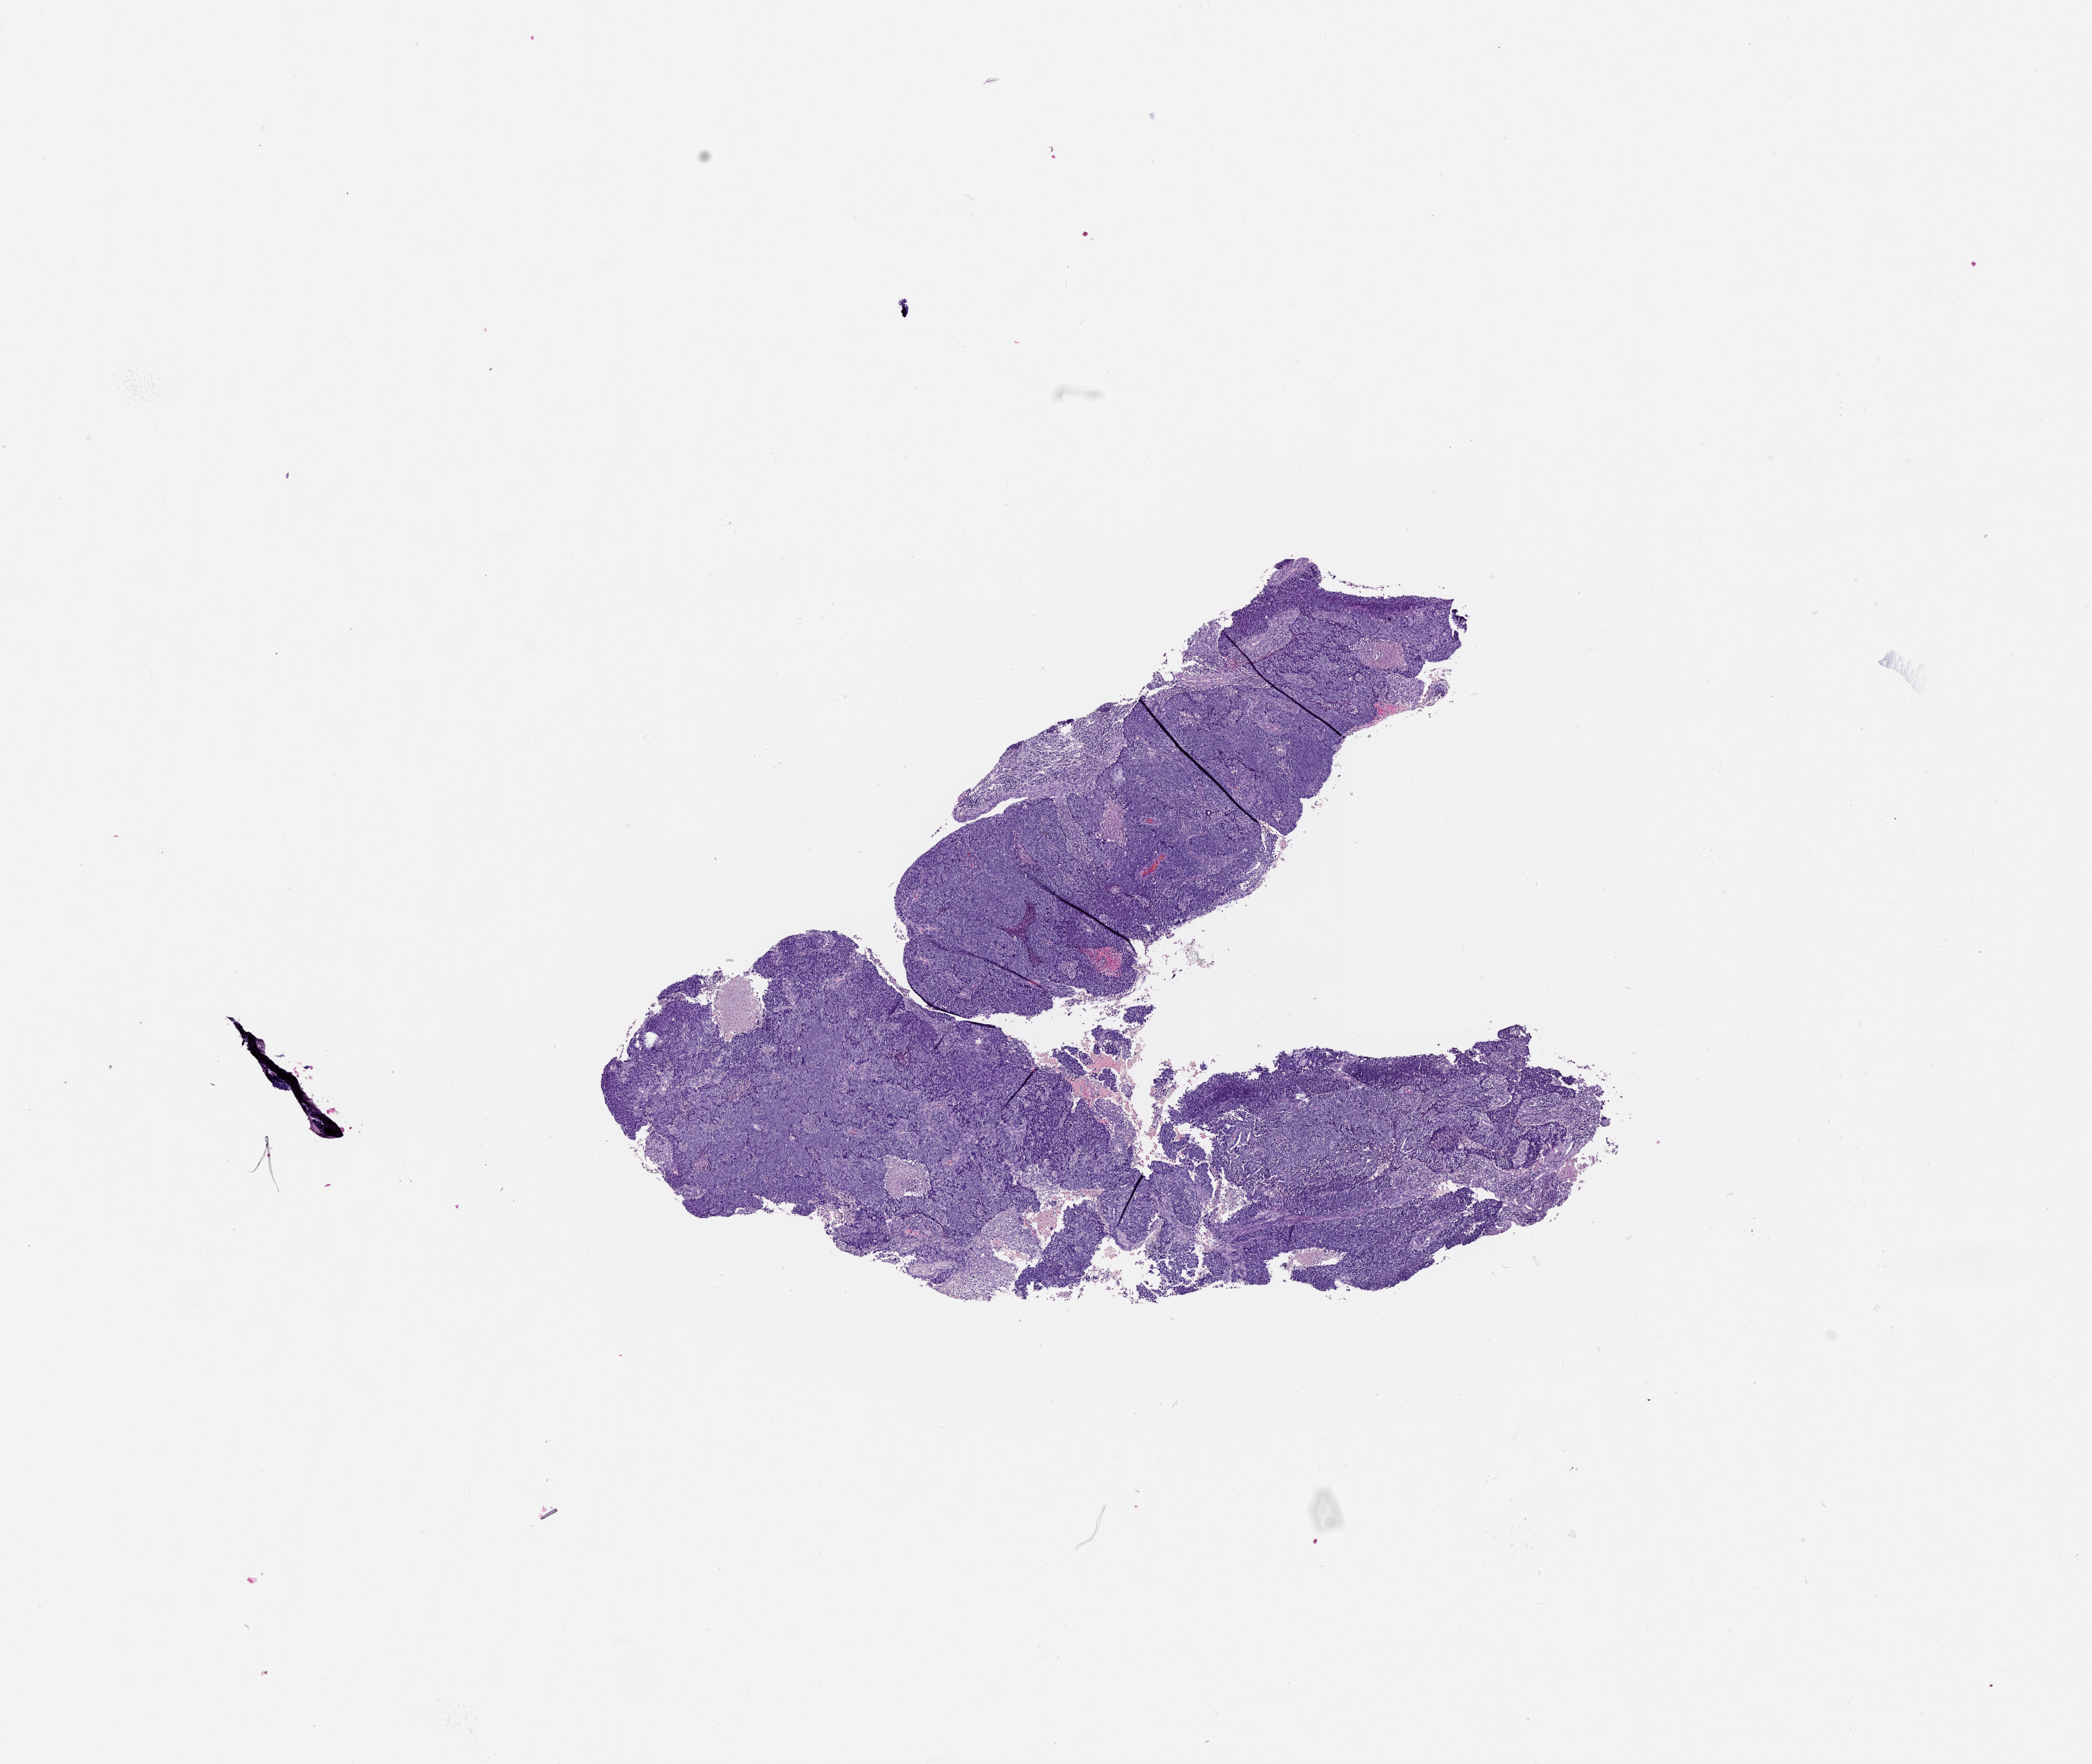
Digitized H&E-stained tissue section (whole slide) — whole scanned area (about 14.0 x 11.8 mm, from a 20x scan) shown as a low-resolution overview; tumour tissue sample, lung. Male, 60 y/o.
Patient diagnosis (cohort enrolment): squamous cell carcinoma (lung).